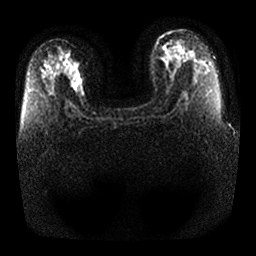
Breast MRI, one axial slice; position 16 of 25 along the scan axis; diffusion-weighted series; image 2 of 4 stored at this slice position (different b-values; order by instance number); 1.5 T; 4 mm slice thickness; 256 × 256 image matrix. Female patient.
Structures marked on this image (expert manual segmentation):
- tumour on diffusion-weighted imaging: bounding box <73,71,84,98> (left, top, right, bottom; pixels)